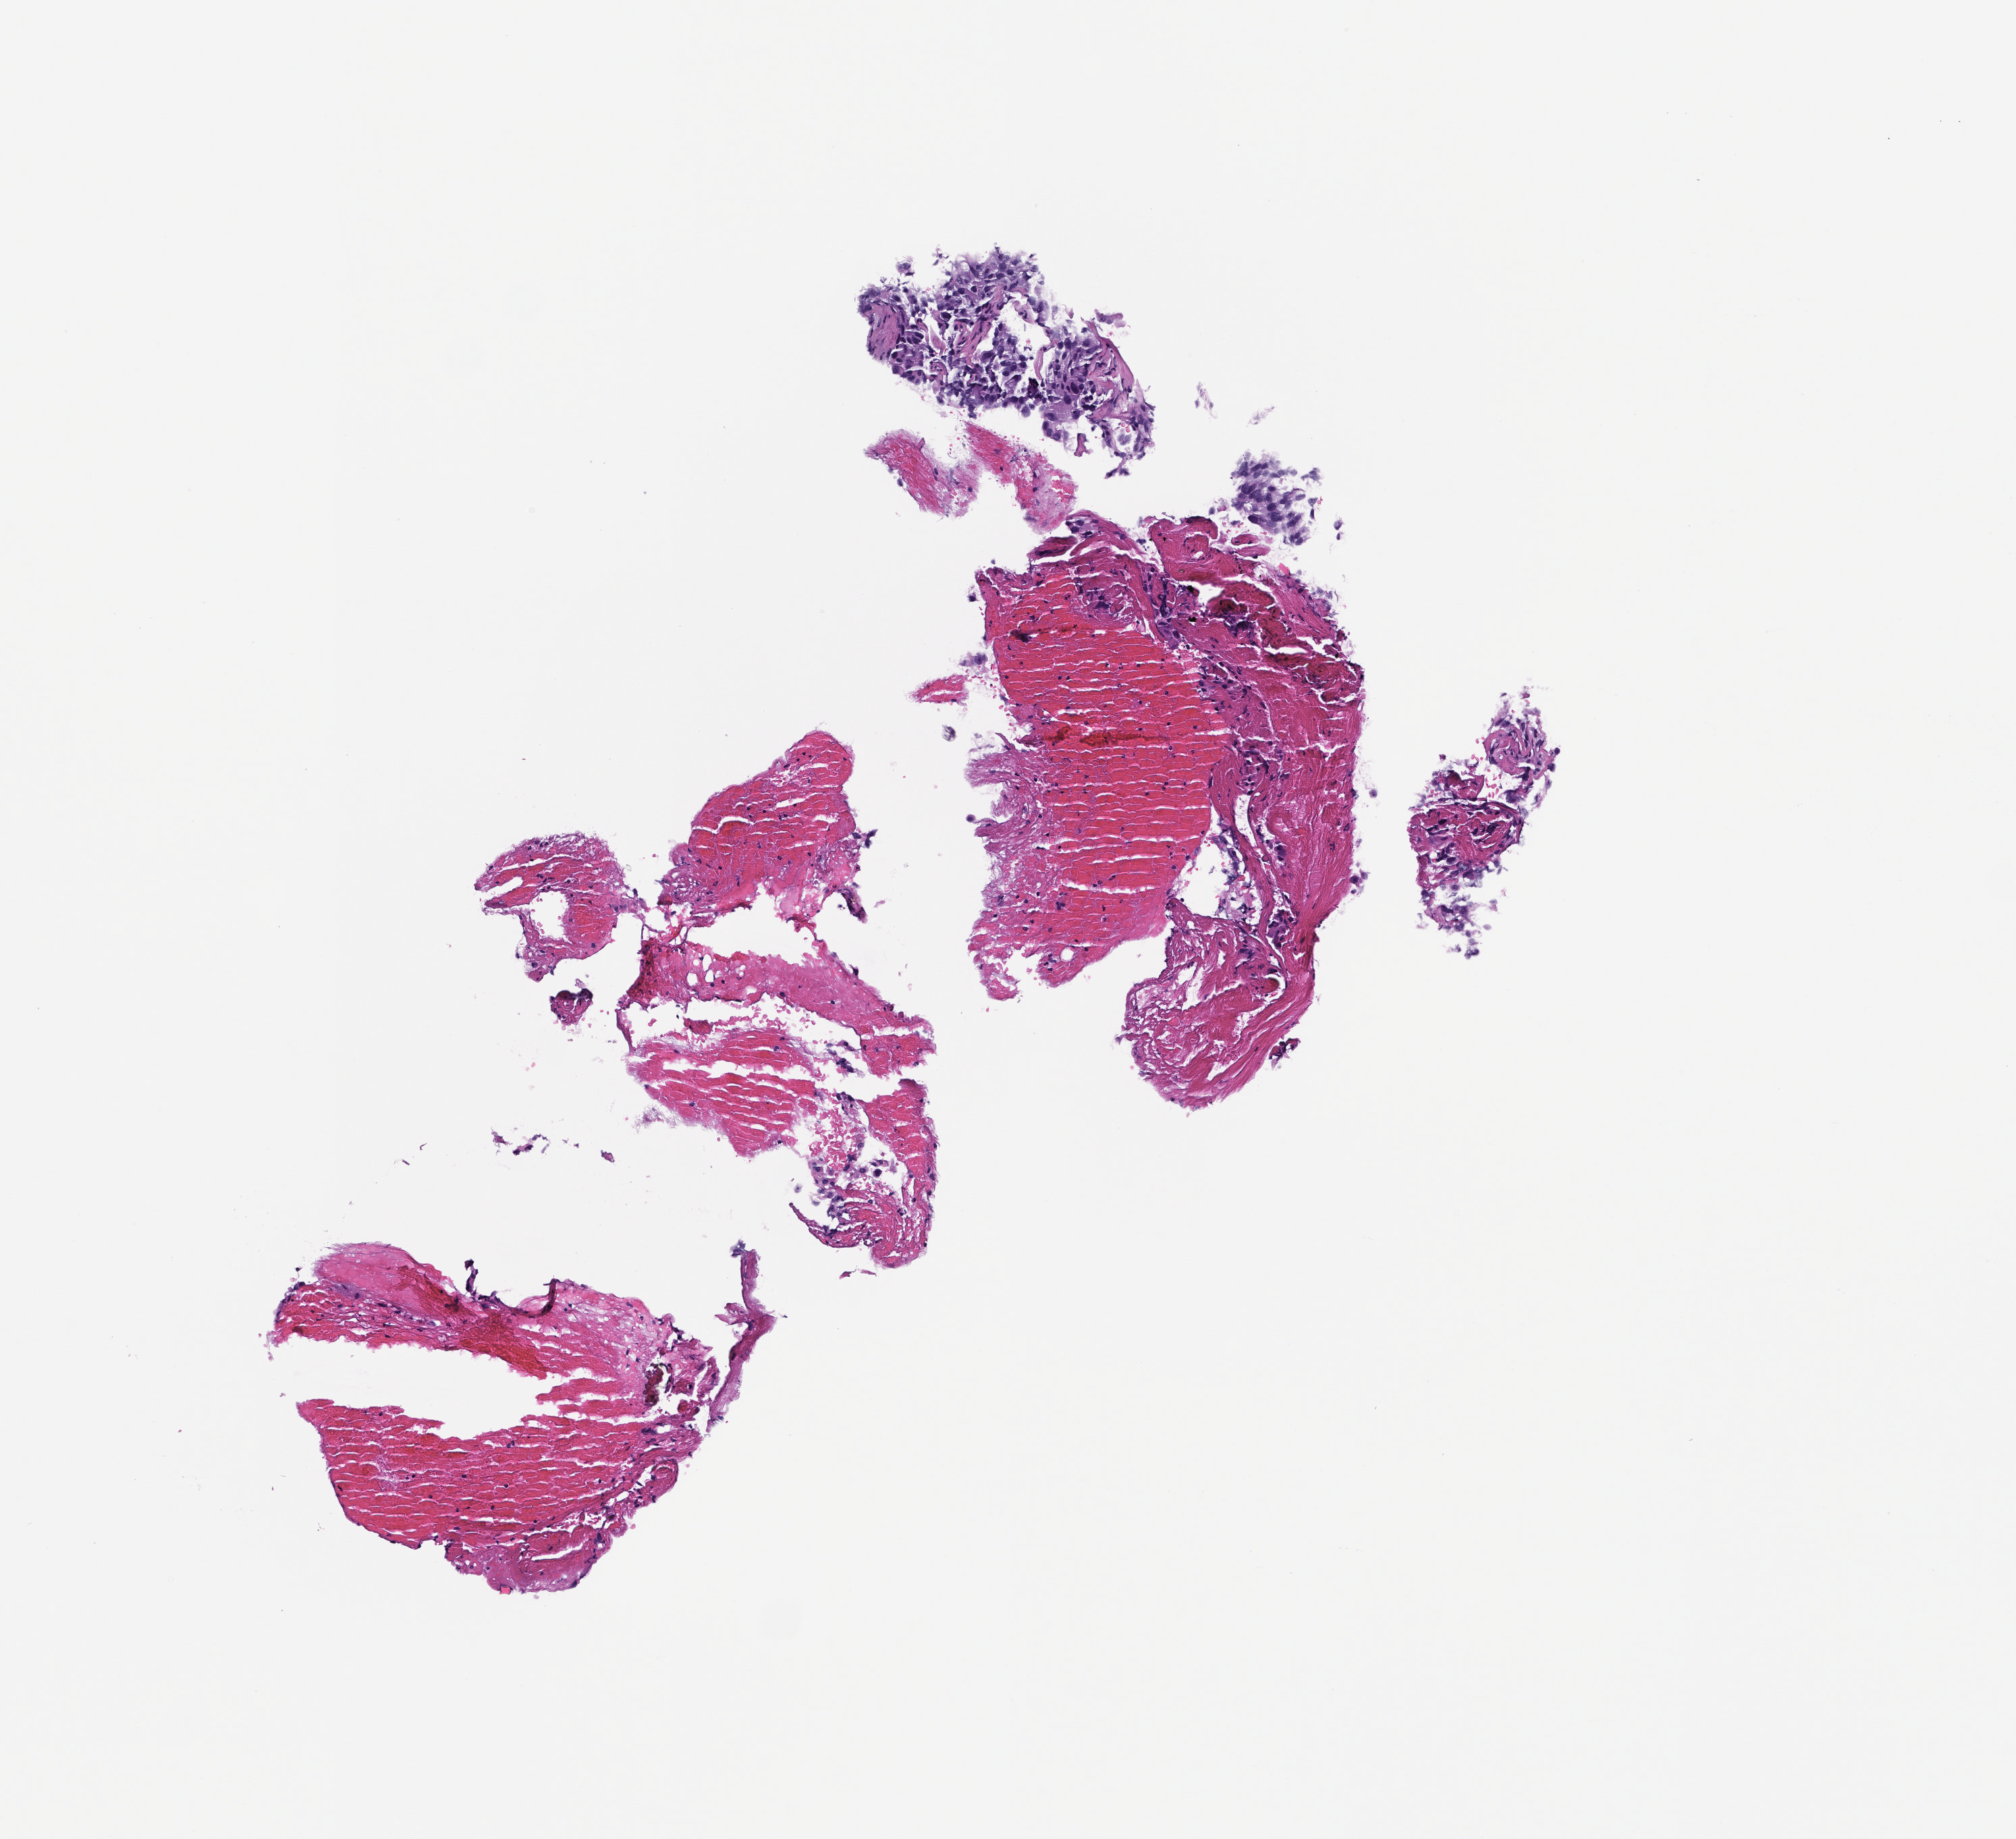
Digitized H&E-stained section — low-resolution overview of the scanned area, about 3.0 x 2.8 mm, FFPE section. Male patient.
• this section: metastatic tumor tissue
• patient diagnosis (primary): Non-Small Cell Lung Carcinoma